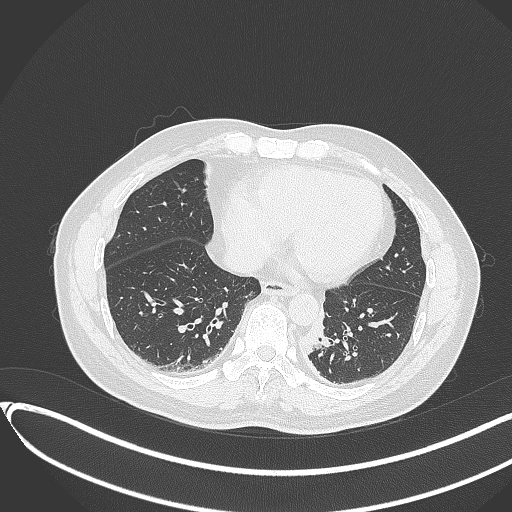
Chest CT, one axial slice. Position 103 of 417 along the scan axis. Reconstruction kernel B70f. 120 kVp. Lung window (W 1500 / L -600 HU). 1 mm slice thickness. 512 × 512 image matrix. Male patient, age 54 years. From the clinical record (not read from this slice): clinical TNM (as recorded): T3 N0 M0.
Annotated regions visible in this slice (bounding box drawn by a radiologist):
- lung tumour (recorded histology: squamous cell carcinoma): bounding box (x1, y1, x2, y2) in pixels: (297, 296, 333, 356)